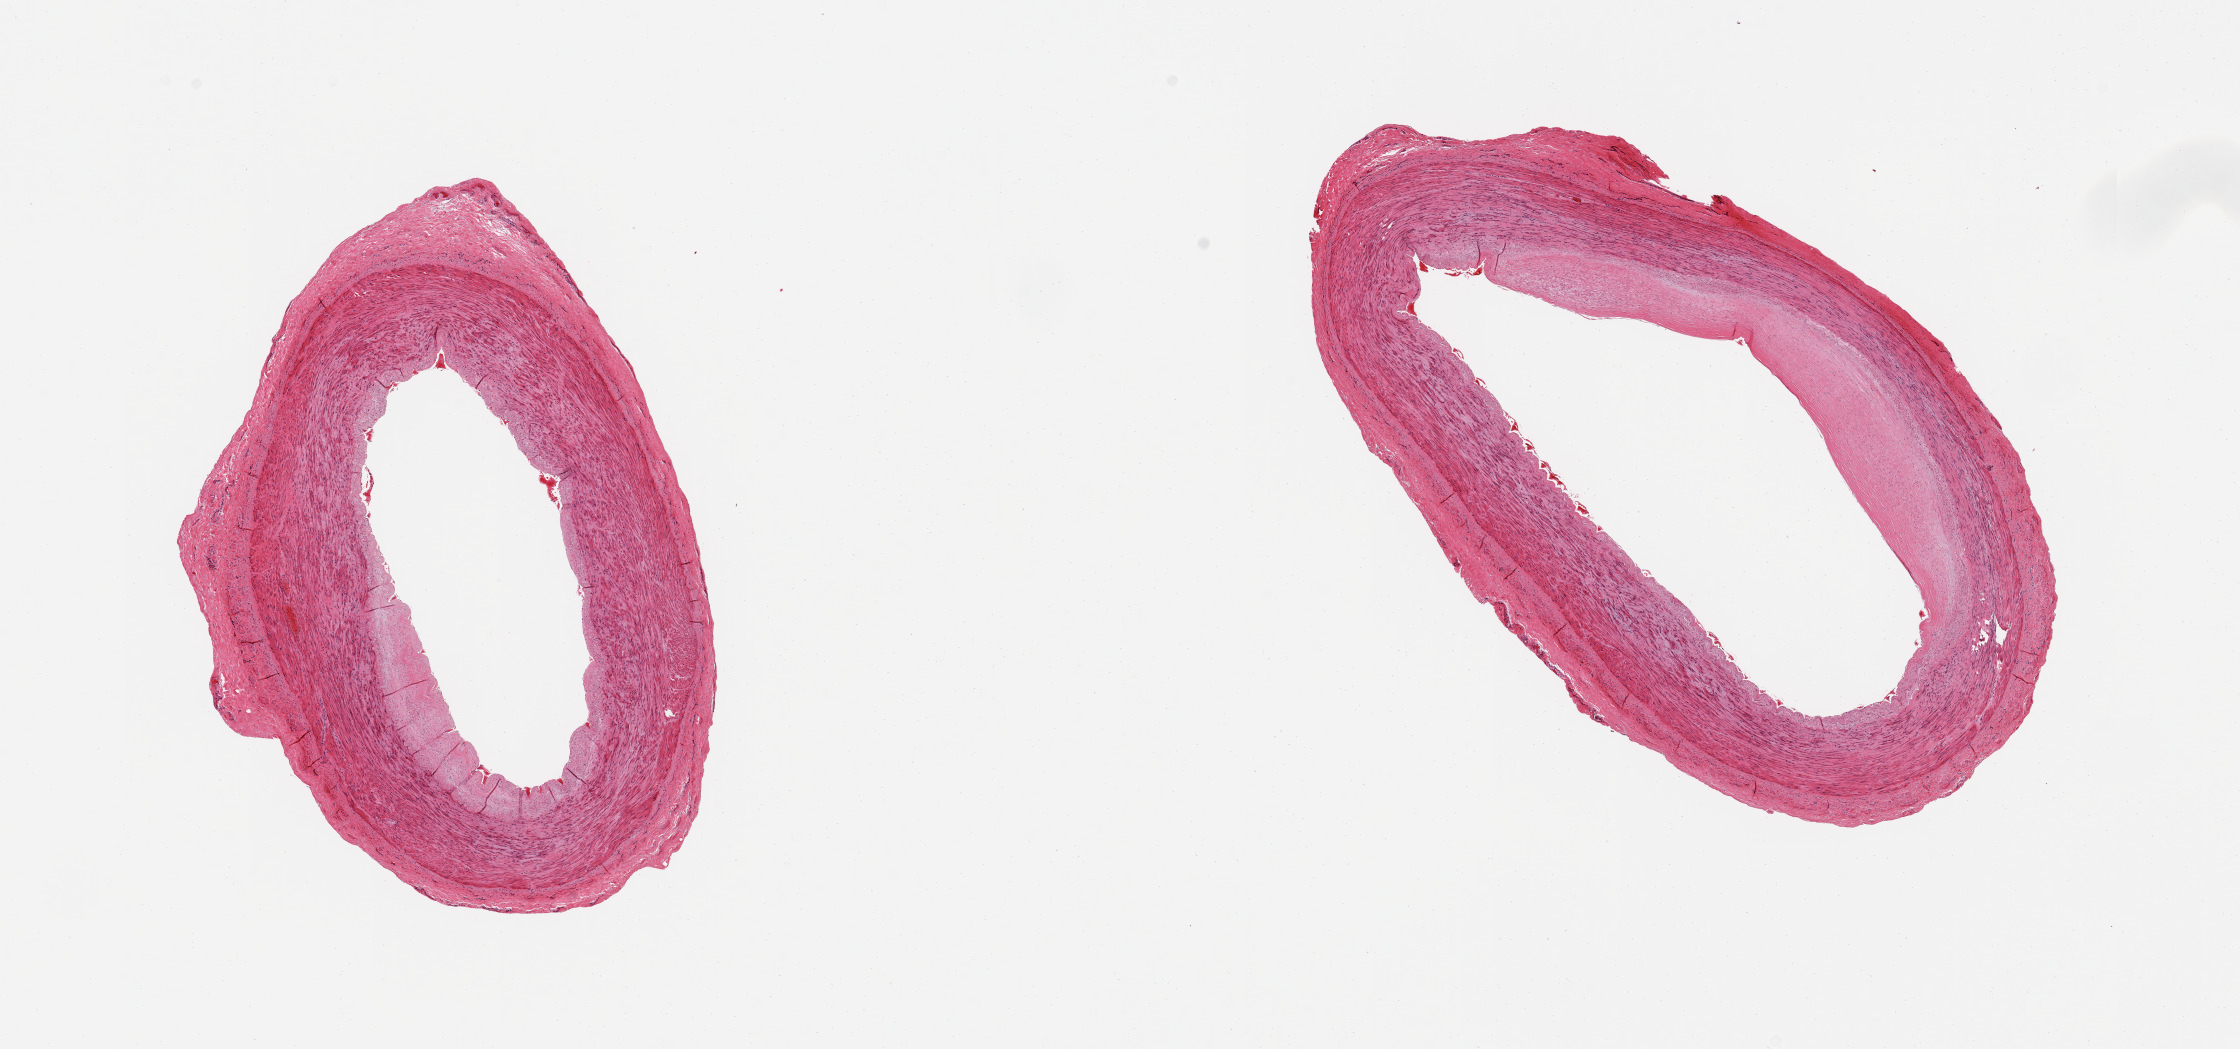
Digitized haematoxylin and eosin-stained section, whole scanned area (about 17.7 x 8.3 mm, slide scanned at 20x) shown as a low-resolution overview; PAXgene-fixed paraffin-embedded (PFPE) section; sampled site (target tissue): tibial artery; donor tissue sample.
- reviewer comment on this tissue sample: 2 pieces; moderate atherosclerosis; well trimmed